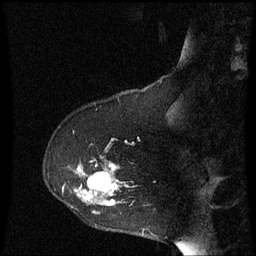
Breast MRI (dynamic contrast-enhanced), one sagittal slice; slice 17 of 60 in the series (ordered by position); dynamic contrast-enhanced series, image 2 of 3 at this slice position (ordered by acquisition); 1.5 T; TE 4.2 ms, TR 8.9 ms; 256 × 256 image matrix, field of view 200 × 200 mm. Patient: female, 53 years. Case-level facts recorded for this patient, not image findings: setting: breast cancer imaged before/during neoadjuvant chemotherapy; receptor status: HR-positive, HER2-negative.
Annotated regions visible in this slice (semi-automatic segmentation, software-assisted and operator-edited):
- analysis volume of interest (the breast-tissue region the enhancement analysis was run in; not a lesion): bounding box (x1, y1, x2, y2) in pixels: (58, 144, 129, 229)
- tumour enhancement mask (voxels above the 70 % enhancement threshold inside the analysis volume of interest): (78, 164, 117, 205)